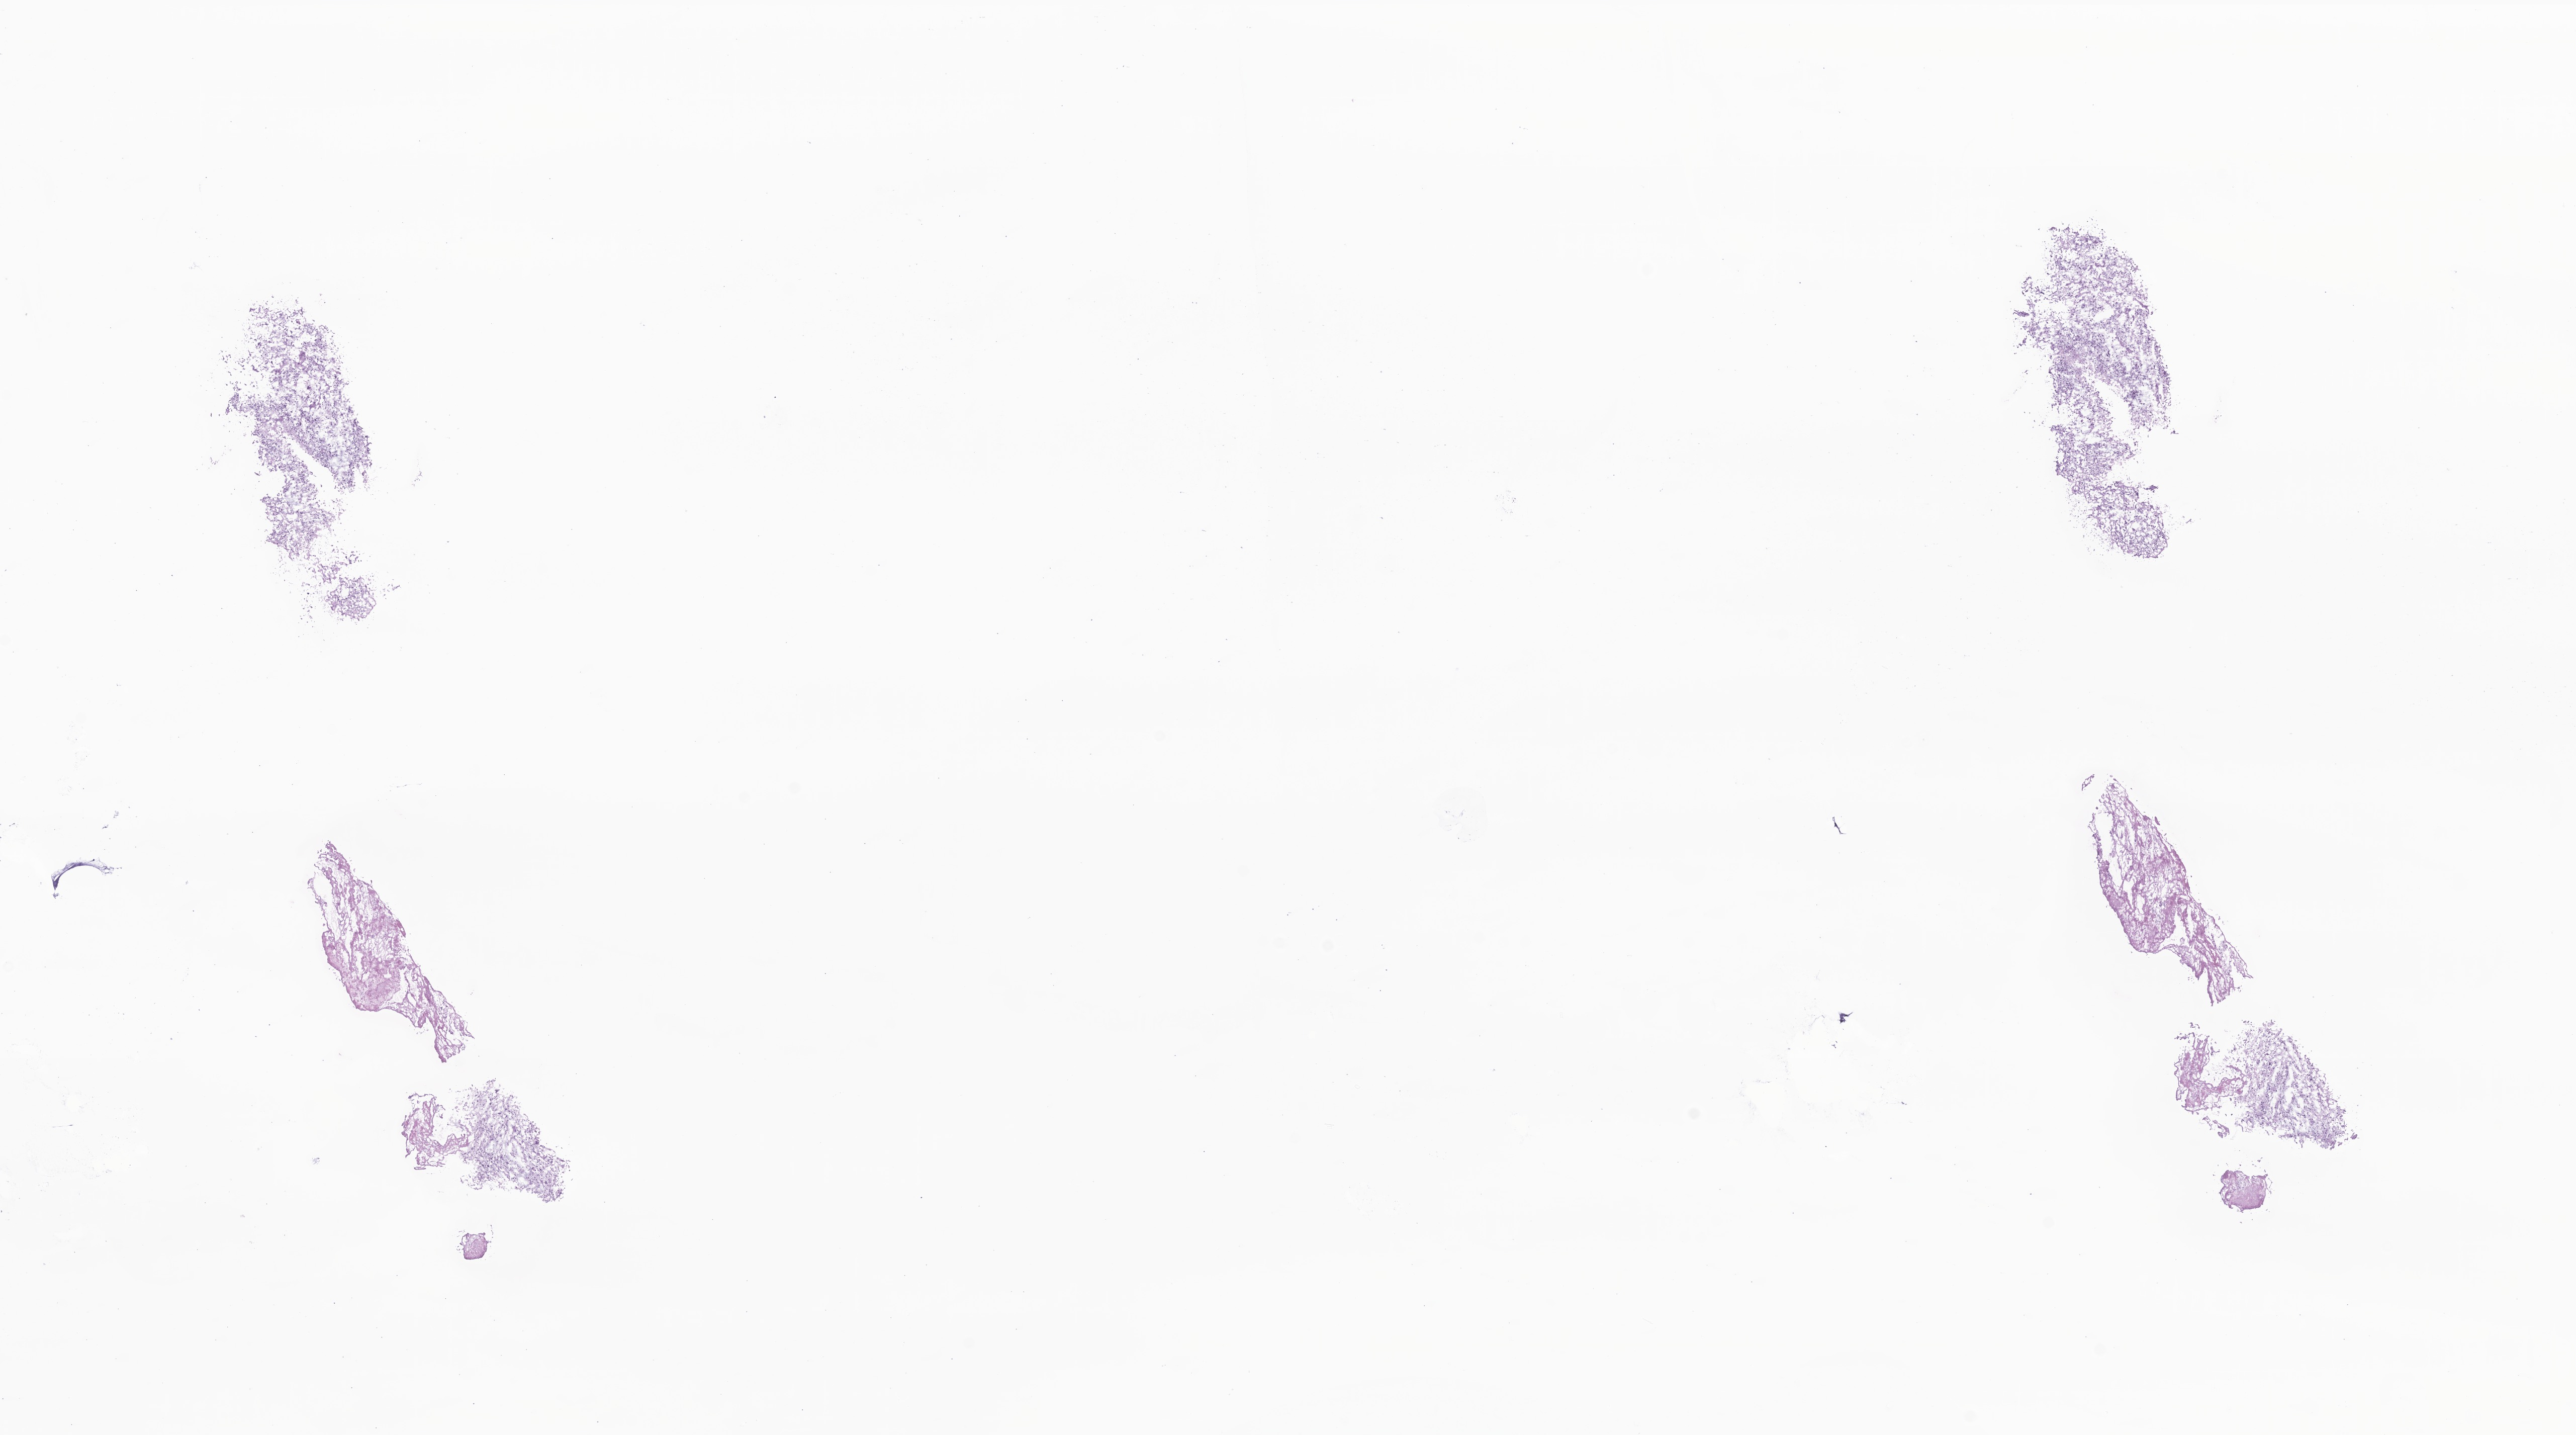
Whole-slide image, H&E stain of tumor tissue from the cerebellum, low-resolution overview of the scanned area, about 21.6 x 12.0 mm, frozen section (OCT-embedded). Patient male; age 59 months (4 years 11 months).
Diagnosis: Glioma, malignant.